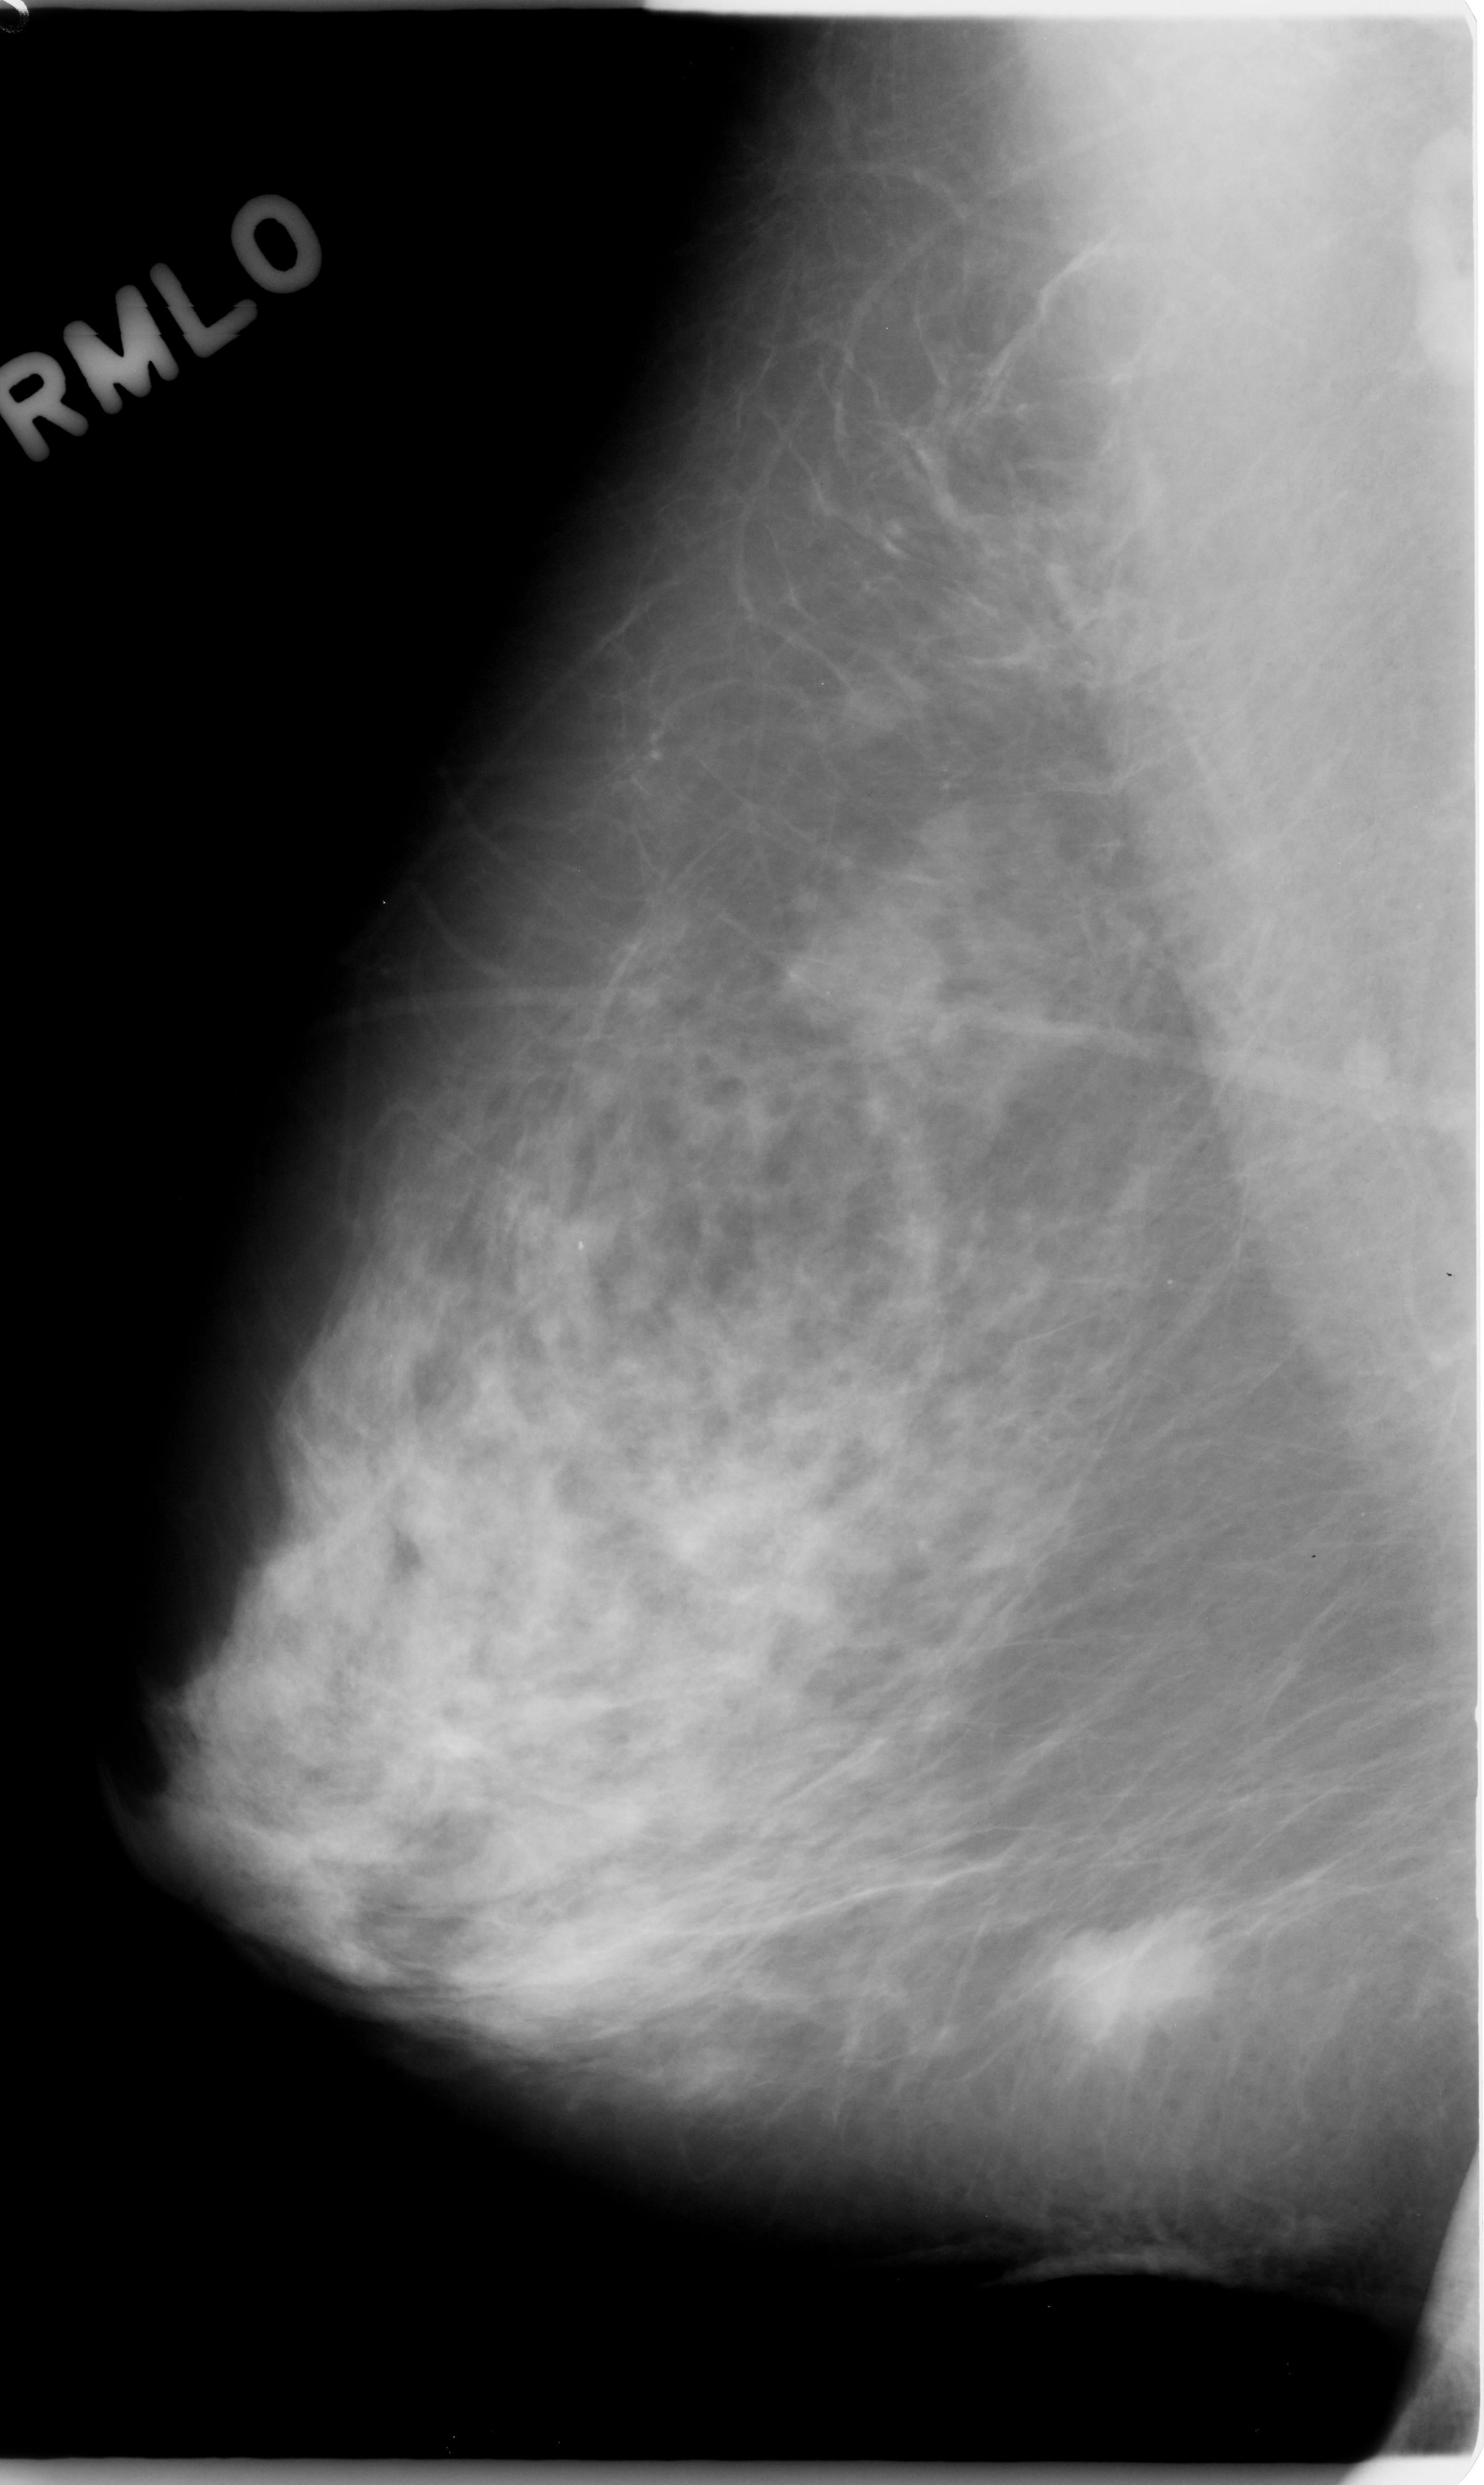
Scanned film-screen mammogram, right breast, mediolateral oblique (MLO) view, breast composition: scattered fibroglandular densities (BI-RADS density category 2 of 4).
- Abnormality record for this image: mass, shape irregular, margins spiculated; BI-RADS assessment category 5; pathology result (as recorded, not read from the image): malignant.